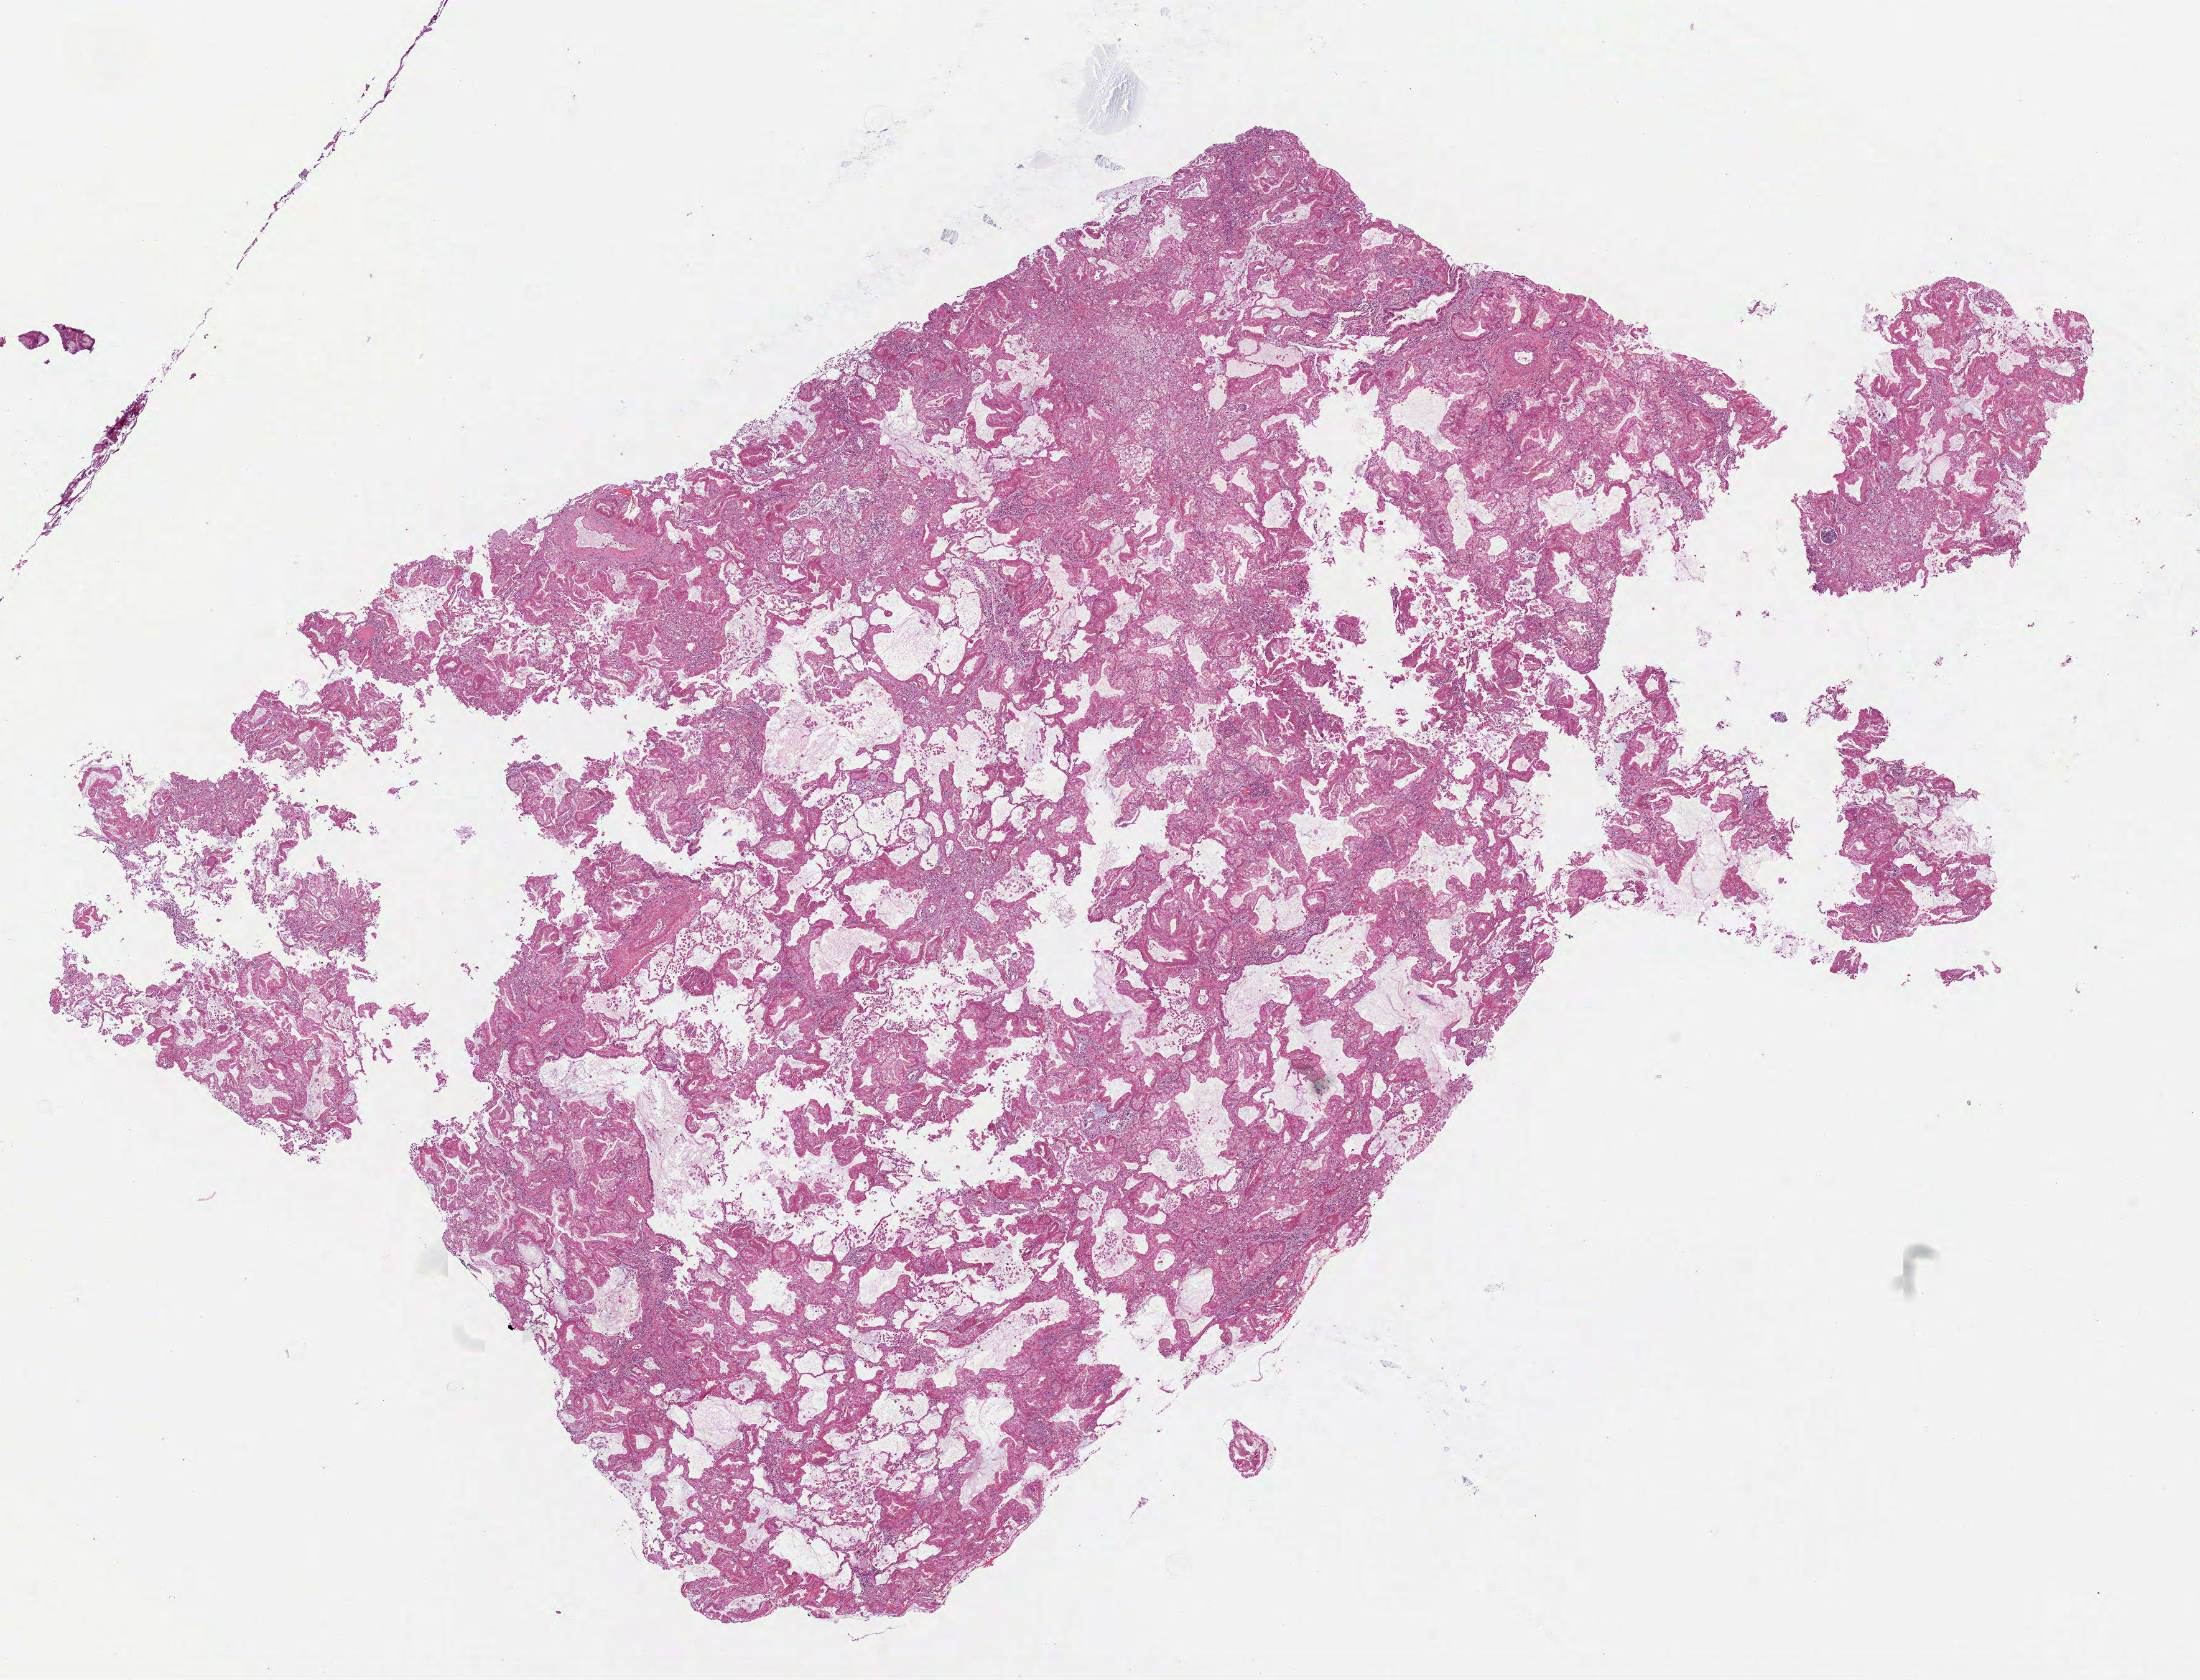
Whole-slide histology image, Hematoxylin and eosin (H&E) stained — whole scanned area (about 14.3 x 10.9 mm, slide scanned at 40x) shown as a low-resolution overview; formalin-fixed paraffin-embedded (FFPE) diagnostic section; primary tumour sample from the lung. Patient: female, age at initial diagnosis 77 years.
* AJCC pathologic stage: IIB (7th edition)
* TNM: T3 N0 MX
* pathologic diagnosis: Mucinous adenocarcinoma (lower lobe, lung)